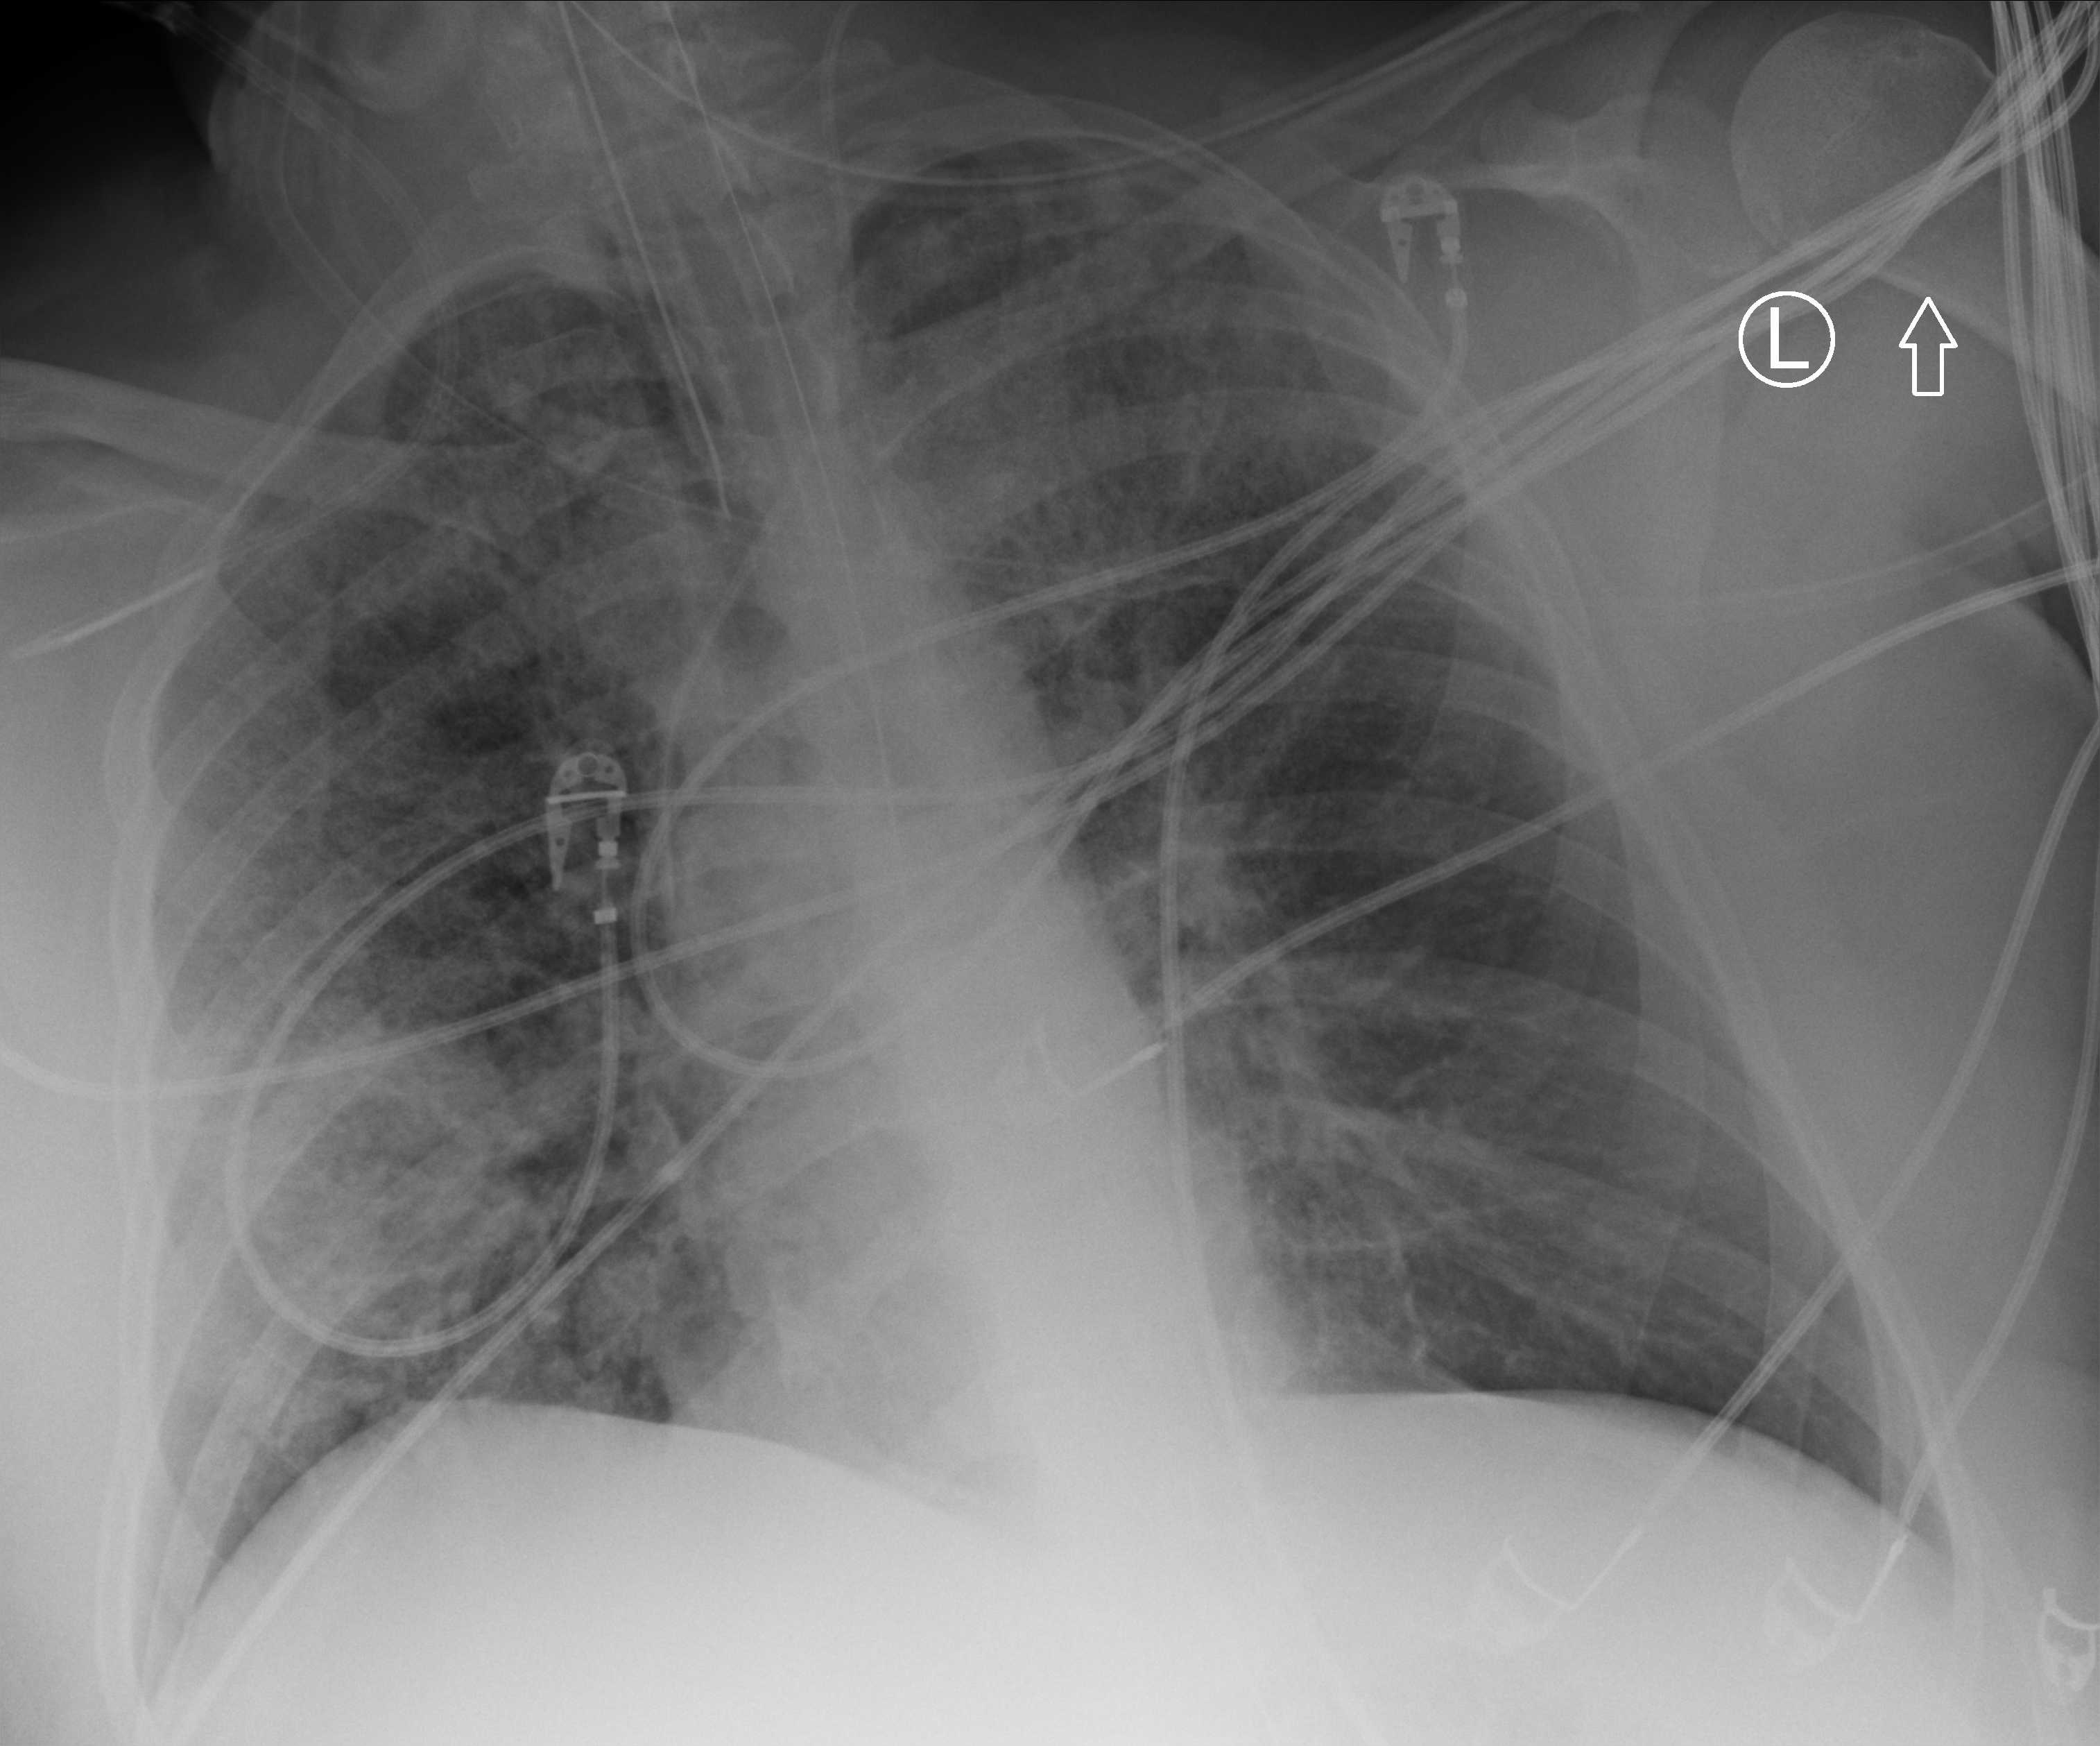
Chest X-ray (portable); anteroposterior (AP) projection. Patient hospitalised with COVID-19, aged 18–59 years.
Admission-level facts for this patient (not findings on this image; timing relative to this image not recorded):
- admitted to intensive care during this hospital stay: yes
- other chronic lung disease (admission record): yes